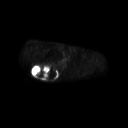
FDG PET of an extremity soft-tissue mass (from a PET/CT study), one axial slice. Slice 195 of 267 in the series (ordered by position). 3.27 mm slice thickness. 128 × 128 image matrix. Patient: male, 61 years. Case-level facts recorded for this patient, not image findings: histological type: pleiomorphic spindle cell undifferentiated; grade: high; site of the primary tumour: right parascapusular.
Structures marked on this image (expert contour drawn on MRI and transferred to this co-registered scan by the dataset authors):
- gross tumour volume including surrounding oedema: bounding box [x1, y1, x2, y2] px = [31, 65, 60, 79]
- gross tumour volume (mass): [31, 65, 57, 78]